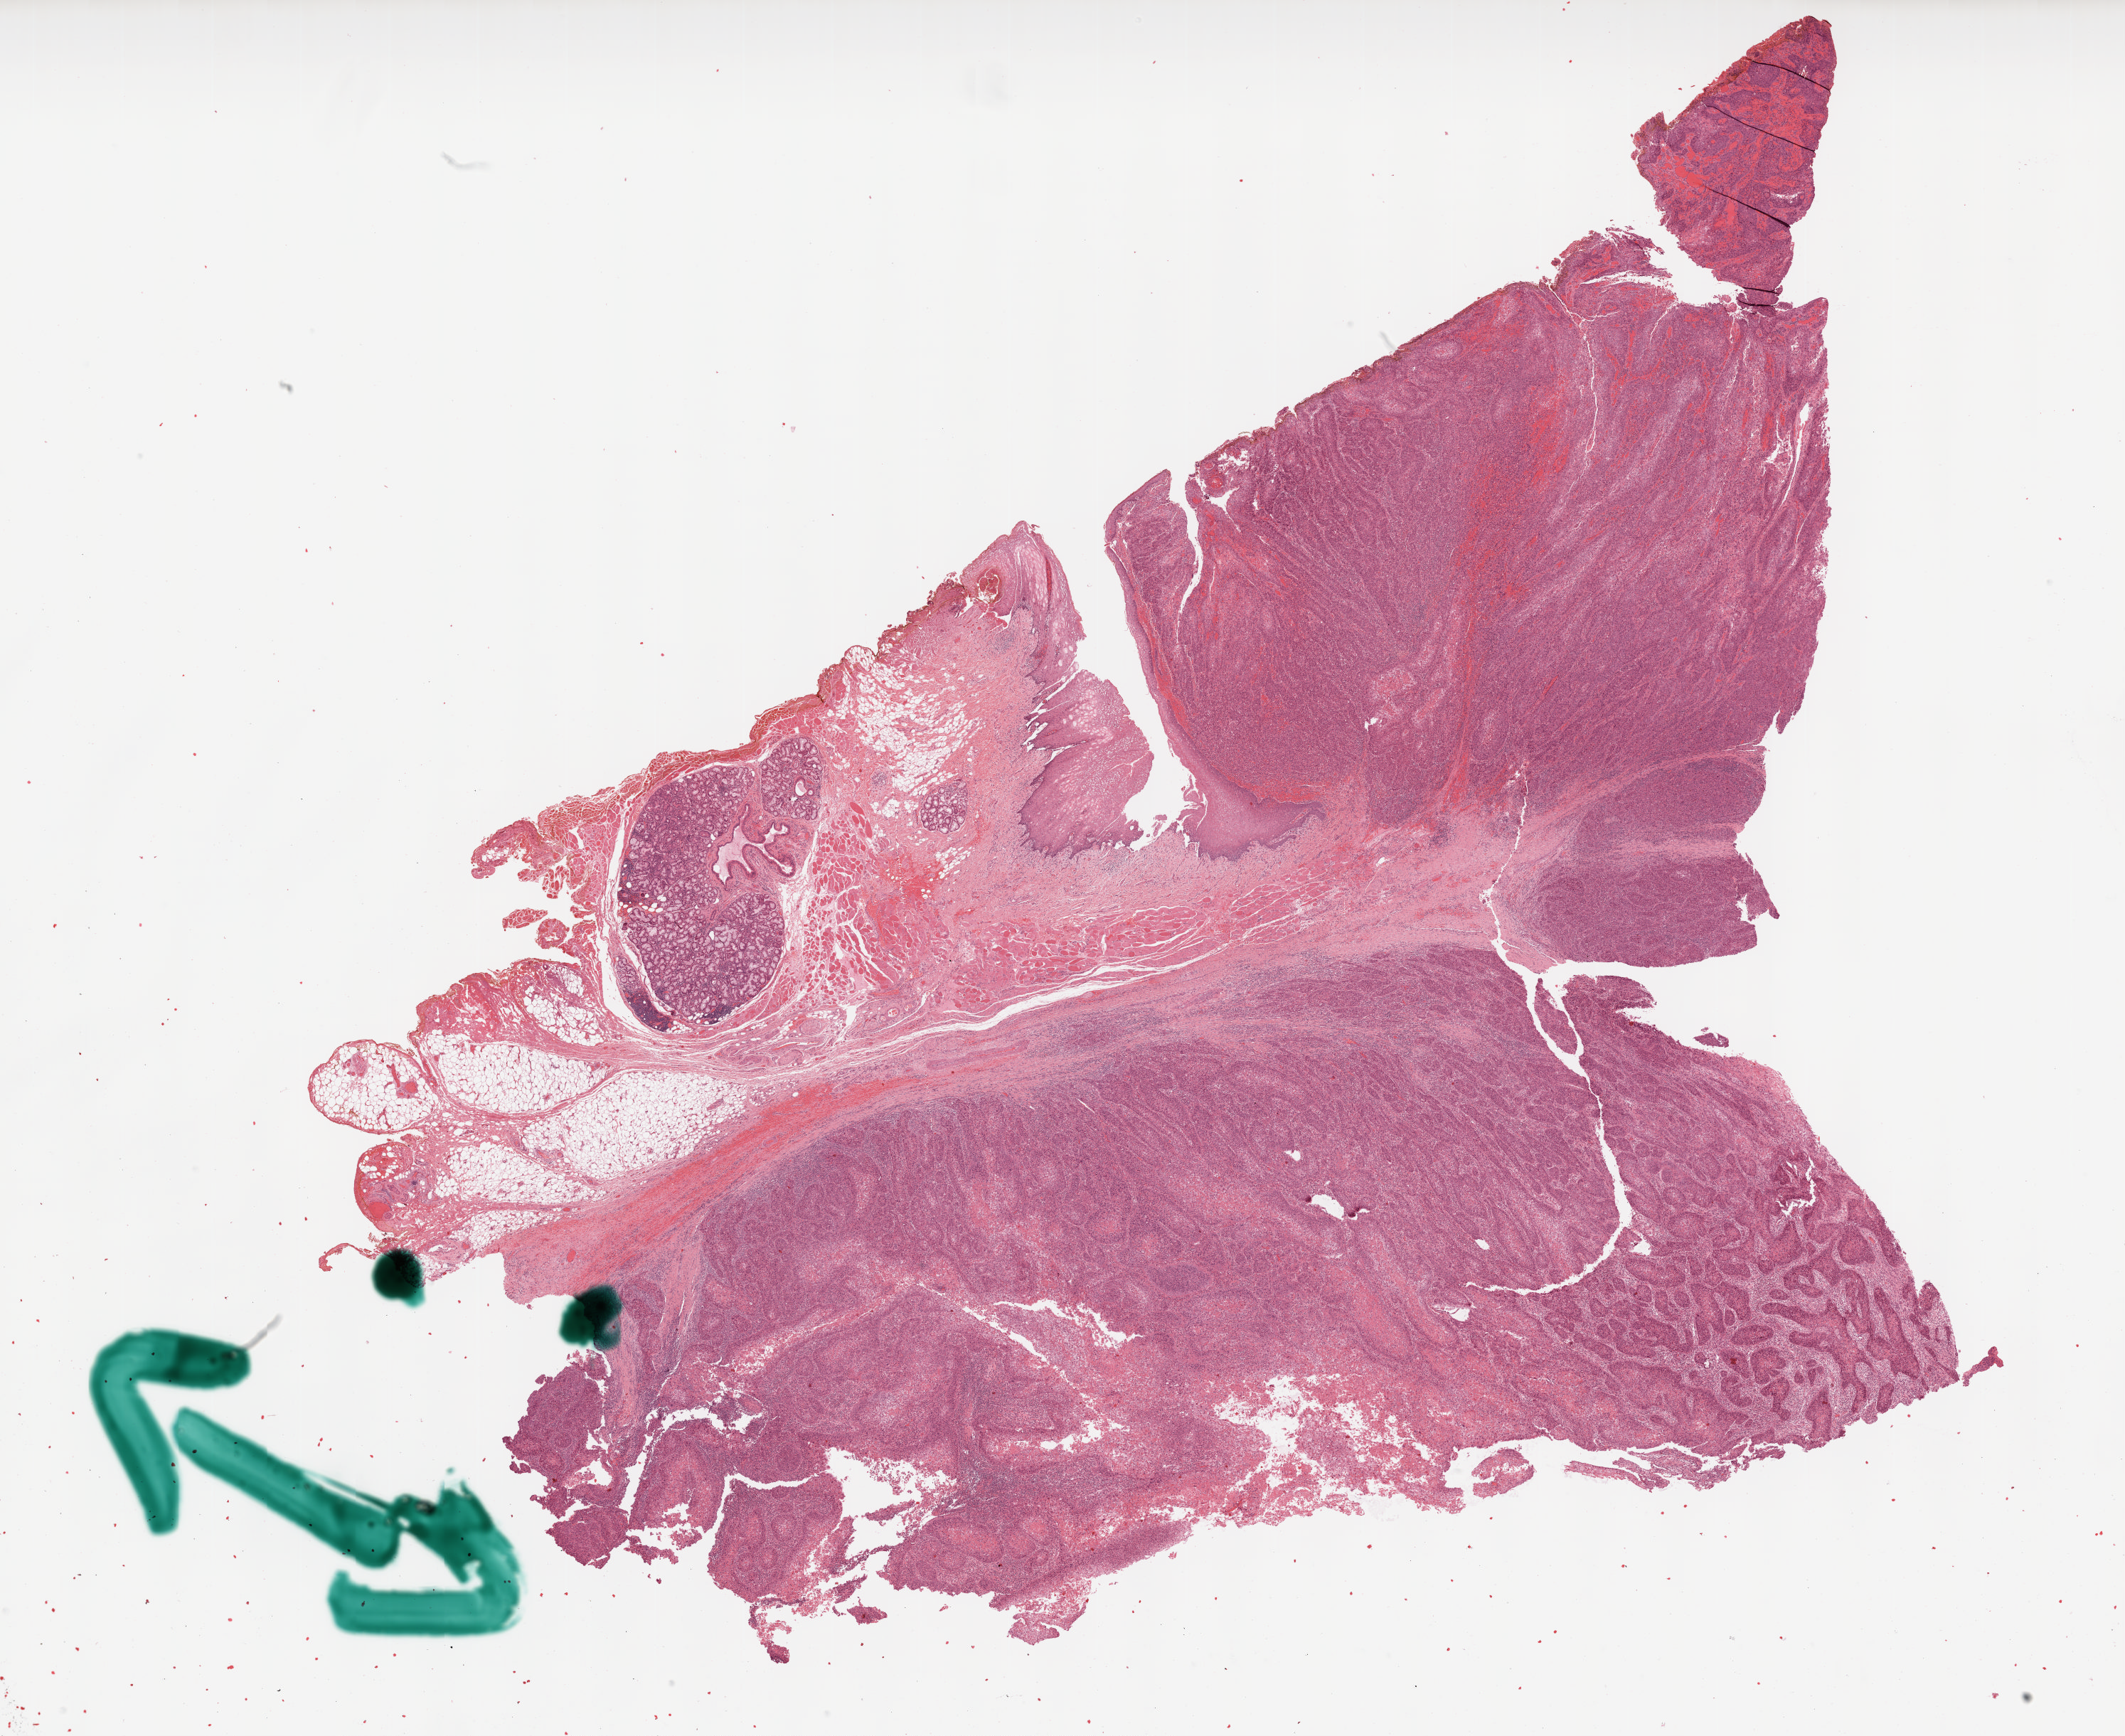
Whole-slide histology image, H&E, a low-resolution overview of the entire scanned area, about 24.0 x 19.6 mm, formalin-fixed paraffin-embedded (FFPE) diagnostic section, sample: primary tumour, head and neck. Male, age 69 years at initial diagnosis.
Histologic diagnosis: Squamous cell carcinoma, NOS.